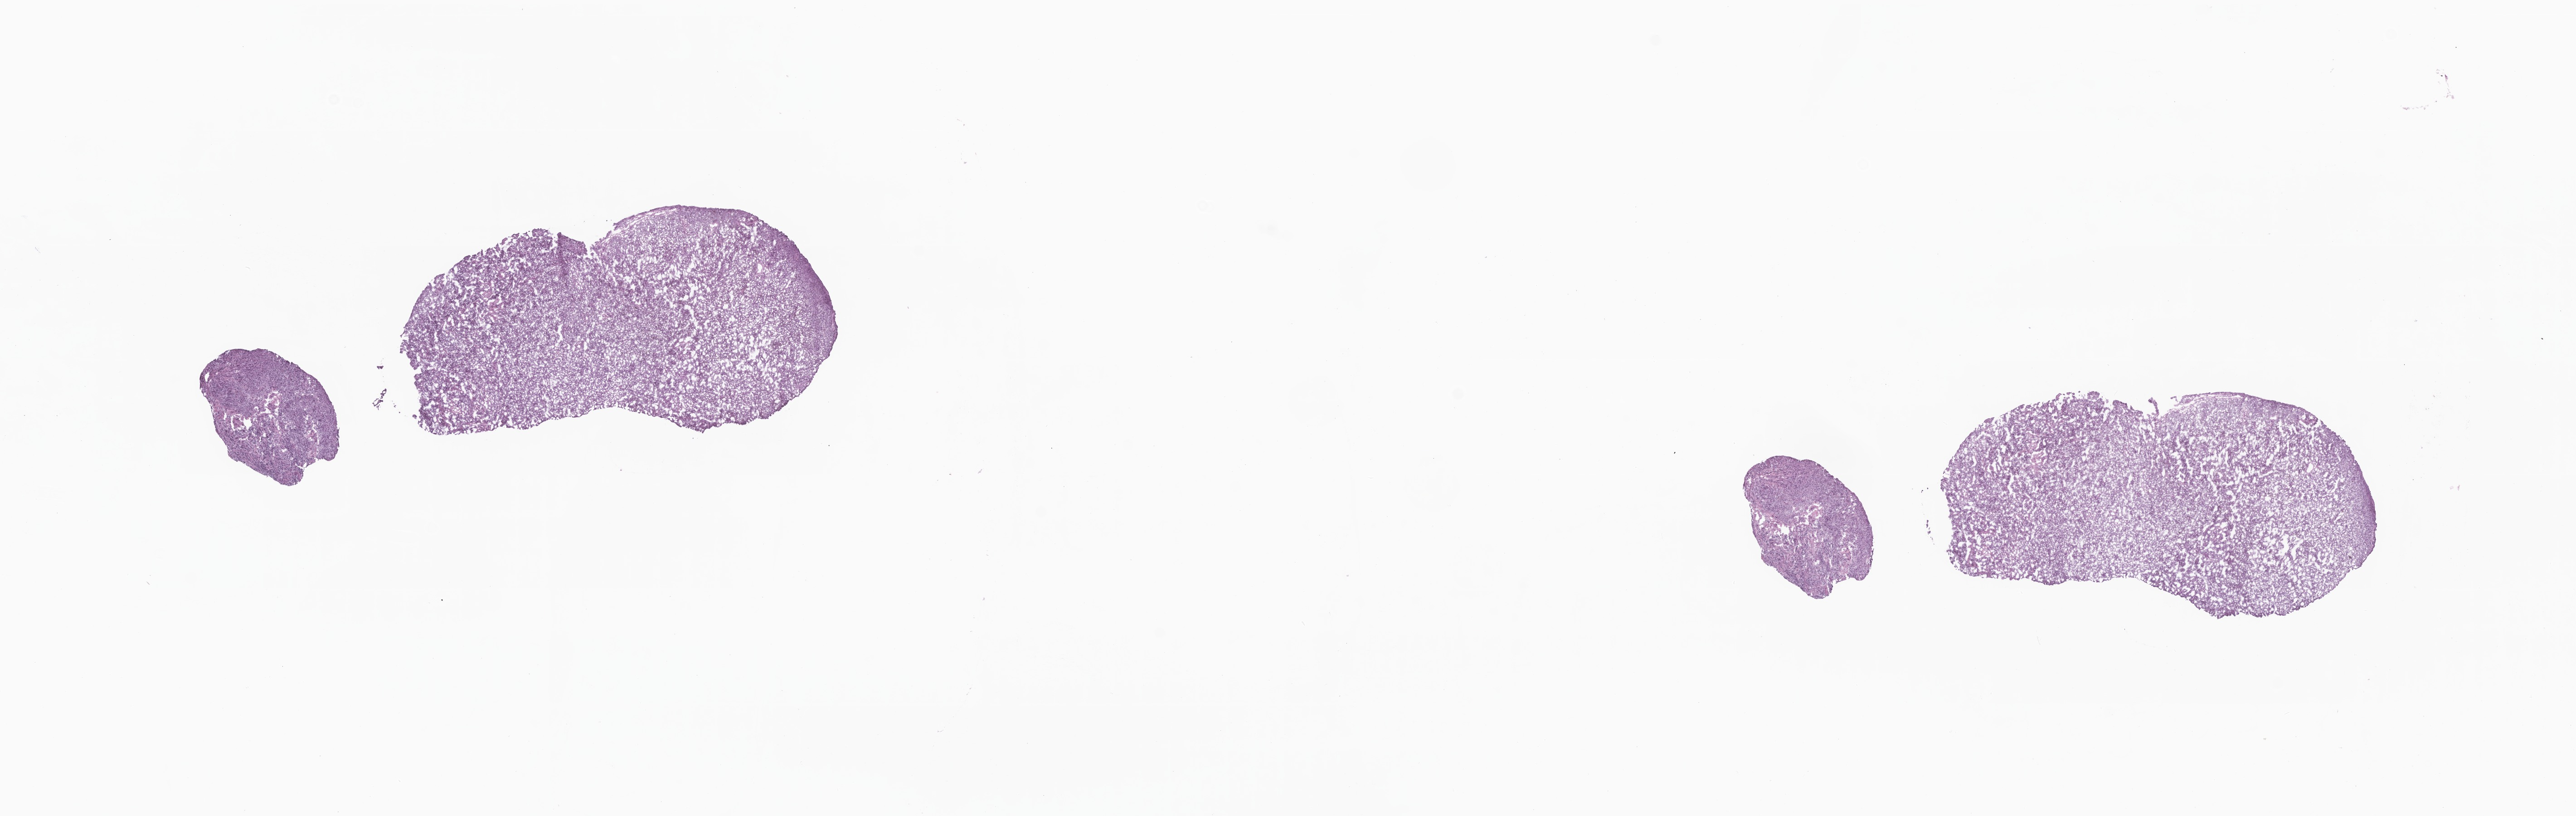
H&E whole-slide image, shown as a low-resolution overview of the whole scanned area (about 24.0 x 7.6 mm). Frozen section (tissue freezing medium). Metastatic tumor tissue, resected from brain. Female patient; age at initial diagnosis 59 years.
Patient diagnosis (primary): Malignant melanoma, NOS.